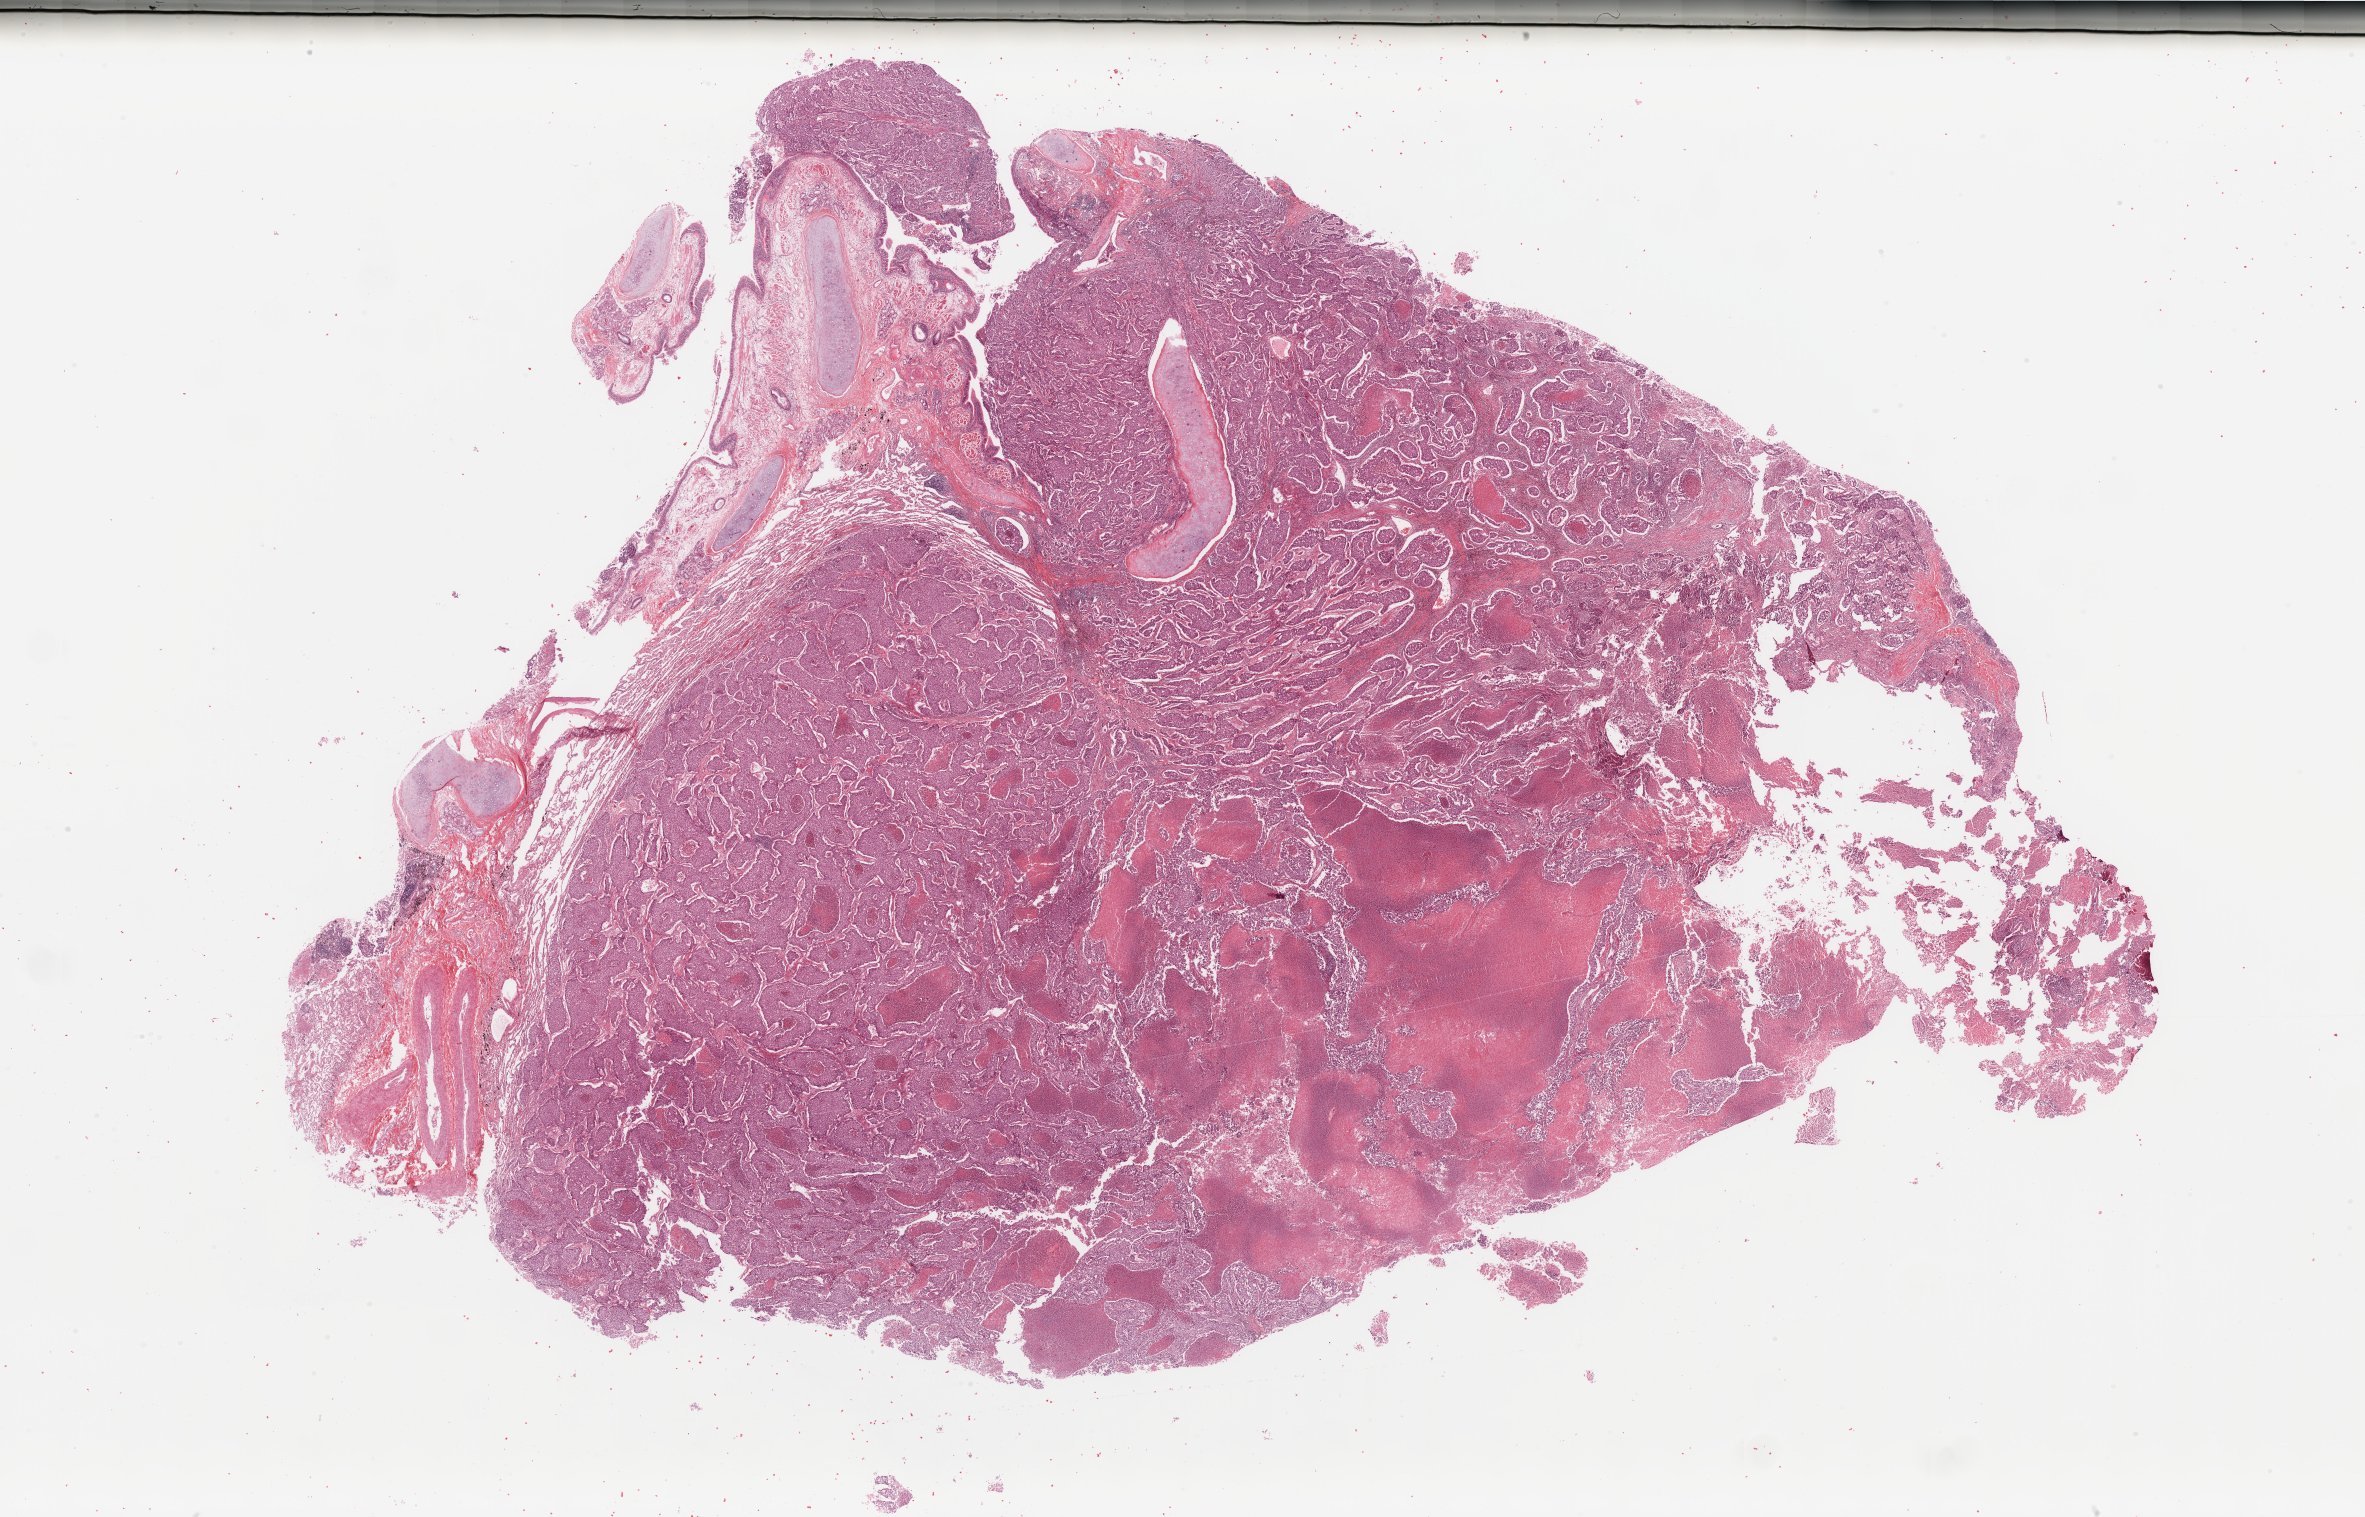
Digitized Hematoxylin and eosin (H&E) stained tissue section (whole slide) — whole scanned area (about 37.4 x 24.0 mm, slide scanned at 20x) shown as a low-resolution overview. Tumour tissue sample, lung. 45-year-old male patient. Histologic grade: G3 (poorly differentiated).
• AJCC pathologic stage: IIB
• histologic diagnosis: Adenocarcinoma, NOS